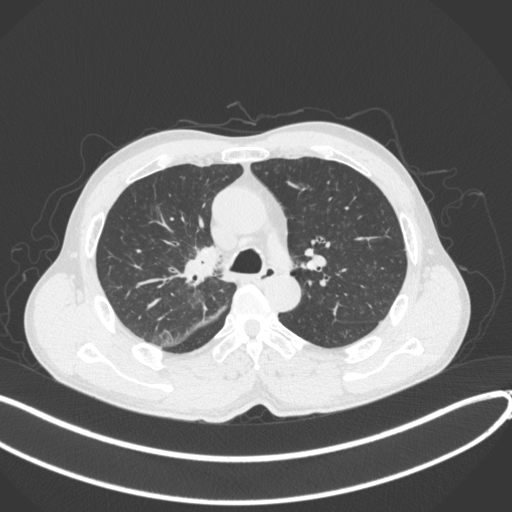
Chest CT, one axial slice. Slice 261 of 409 in the series (ordered by position). Reconstruction kernel B31f. Lung window (W 1500 / L -600 HU). 1 mm slice thickness. 512 × 512 image matrix, field of view 400 × 400 mm. Patient: male, 53 years. Case-level facts recorded for this patient, not image findings: clinical TNM (as recorded): T1b N0 M0.
Outlined on this slice (rectangle marked by the reading radiologist):
- lung tumour (recorded histology: squamous cell carcinoma): bounding box <178,245,223,288> (left, top, right, bottom; pixels)